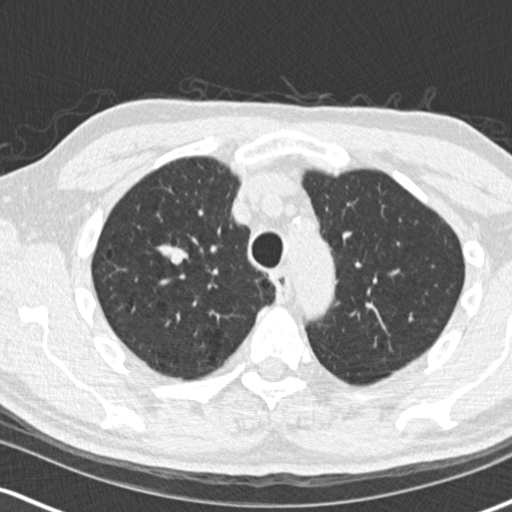
Low-dose screening chest CT, one axial slice; slice 119 of 170 in the series (ordered by position); reconstruction kernel B30f; 120 kVp; lung window (W 1500 / L -600 HU); 2 mm slice thickness; 512 × 512 image matrix, field of view 320 × 320 mm.
Structures marked on this image (expert manual segmentation):
- lesion 1 (tumor, upper lobe of right lung): bounding box (x1, y1, x2, y2) in pixels: (171, 247, 188, 265)